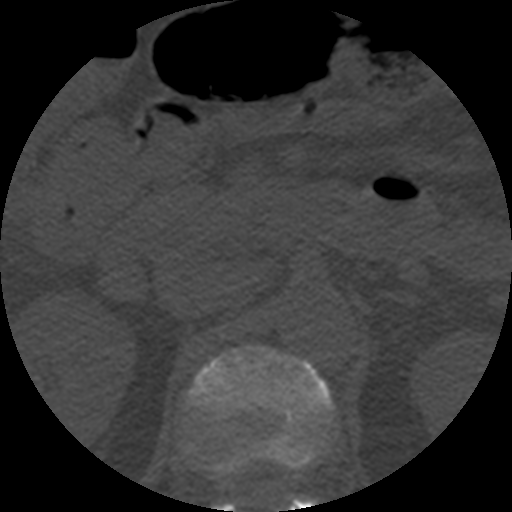
CT including the spine, one axial slice. Slice 198 of 508 in the series (ordered by position). 120 kVp. Bone window (W 1800 / L 400 HU). 1.25 mm slice thickness. 512 × 512 image matrix, field of view 160 × 160 mm. Patient age 57 years. Case-level facts recorded for this patient, not image findings: primary cancer: prostate.
Outlined on this slice (semi-automatic segmentation, software-assisted and operator-edited):
- L1 vertebra: bounding box <186,345,334,512> (left, top, right, bottom; pixels)